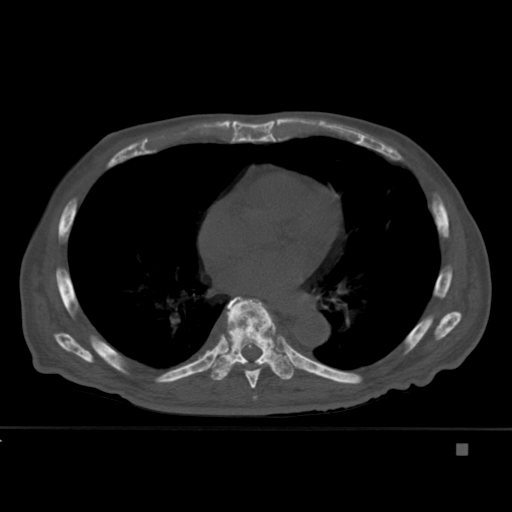
CT including the spine, one axial slice; position 270 of 451 along the scan axis; bone window (W 1800 / L 400 HU); 1.5 mm slice thickness; 512 × 512 image matrix, field of view 378 × 378 mm. Patient: male, 75 years. Case-level facts recorded for this patient, not image findings: primary cancer: prostate.
Structures marked on this image (semi-automatically segmented with operator editing):
- T6 vertebra: bounding box (x1, y1, x2, y2) in pixels: (253, 396, 257, 400)
- T7 vertebra: (244, 299, 276, 389)
- T8 vertebra: (207, 296, 294, 380)